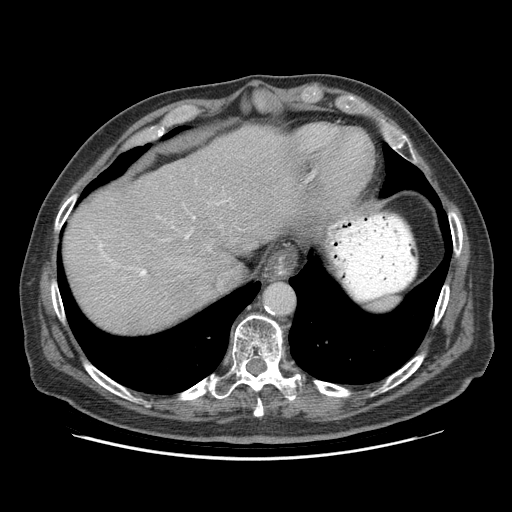
Contrast-enhanced abdominal CT (liver protocol), one axial slice. Slice 74 of 95 in the series (ordered by position). Soft-tissue window (W 400 / L 40 HU). 2.5 mm slice thickness. 512 × 512 image matrix, field of view 400 × 400 mm. Case-level facts recorded for this patient, not image findings: diagnosis: hepatocellular carcinoma (patient treated with transarterial chemoembolisation; whether this scan precedes or follows treatment is not stated here); TNM stage (as recorded): Stage-IVB; Child-Pugh class: A.
Annotated regions visible in this slice (semi-automatic segmentation, software-assisted and operator-edited):
- abdominal aorta: bounding box [x1, y1, x2, y2] px = [265, 283, 293, 313]
- liver parenchyma outside the tumour (the mass and vessels are separate outlines, so this box may not span the whole liver): [64, 124, 295, 332]
- liver vessels: [140, 235, 189, 276]